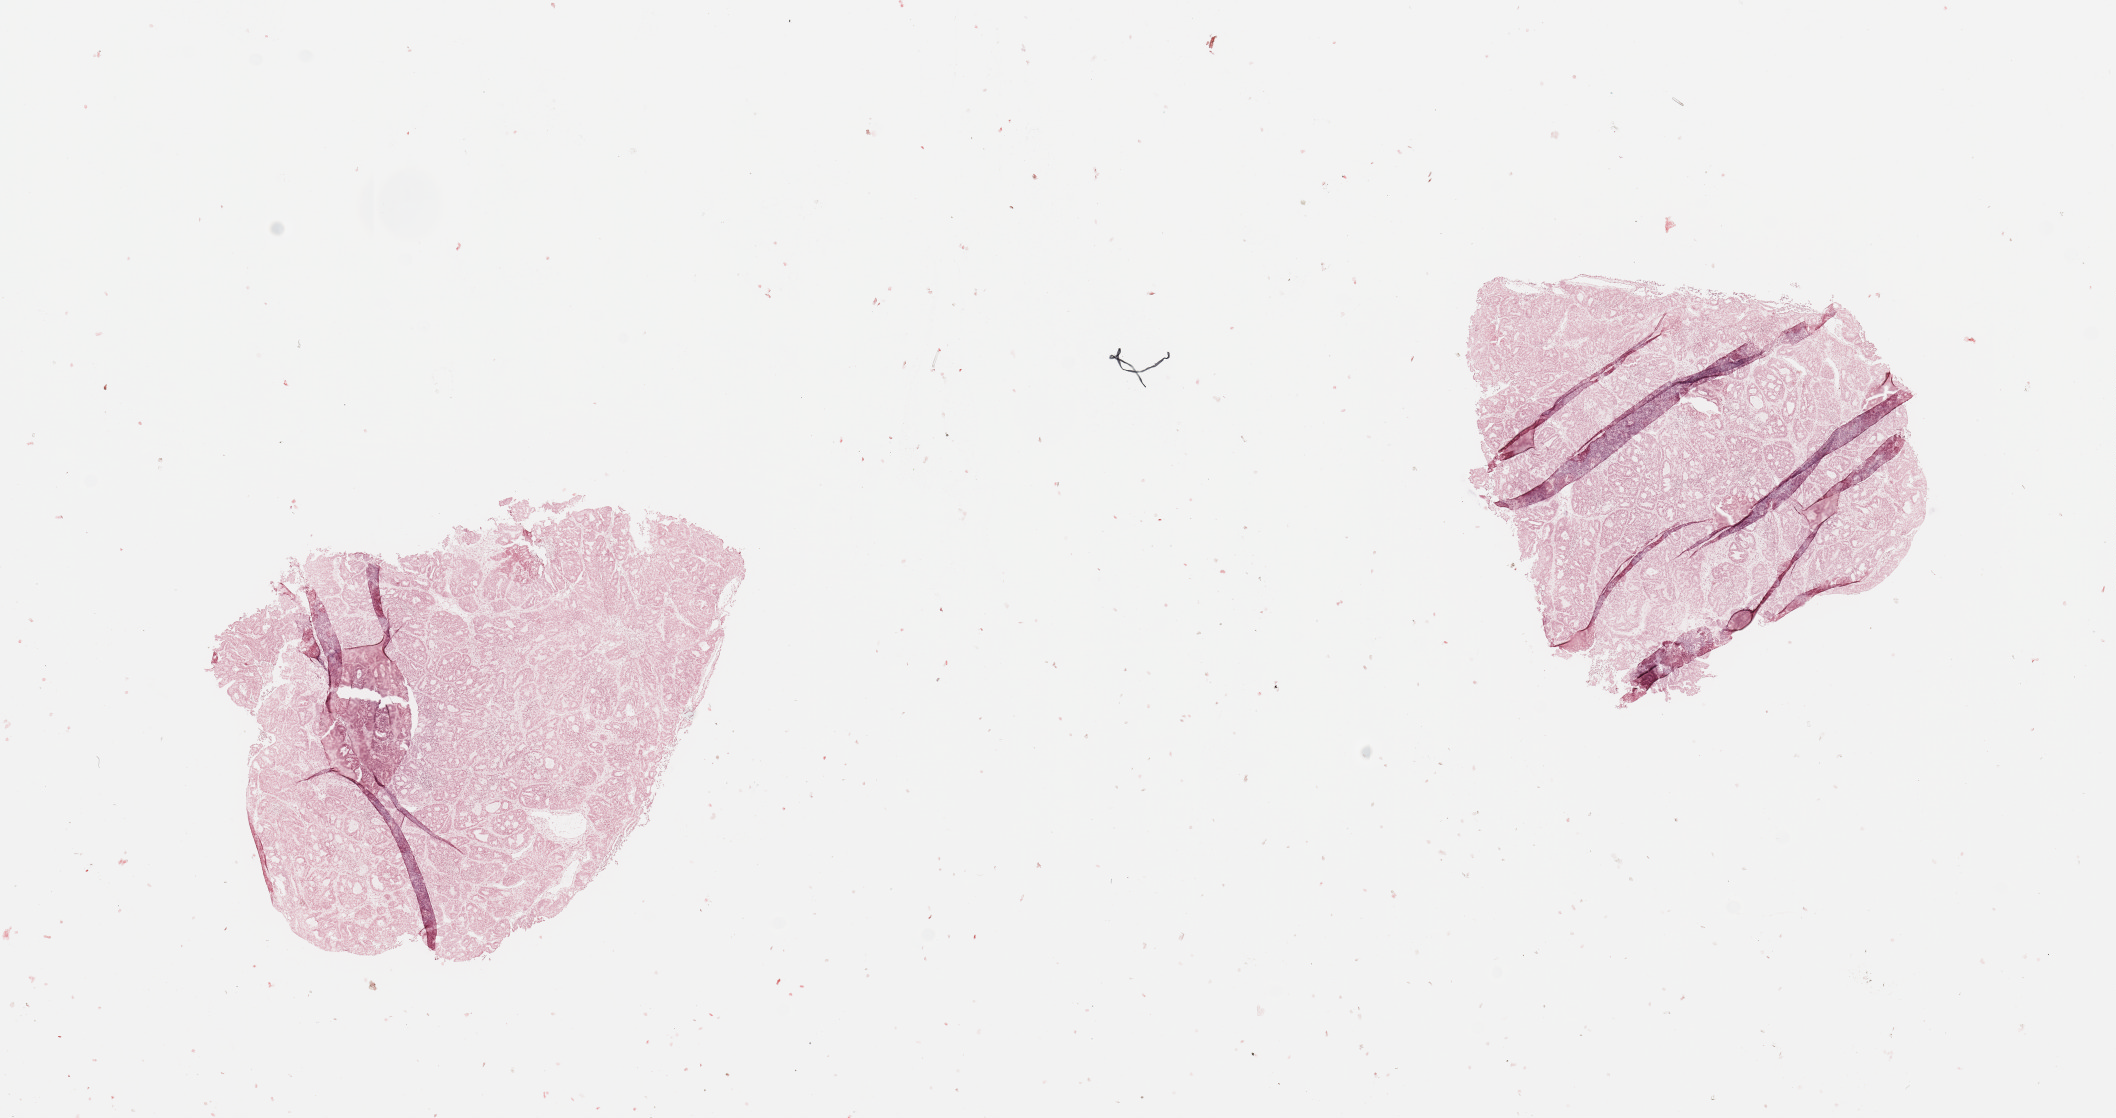
Digitized Hematoxylin and eosin (H&E) stained tissue section (whole slide), whole scanned area (about 16.7 x 8.8 mm, from a 20x scan) shown as a low-resolution overview; tumour tissue sample, sampled site: uterus. Patient: female, age 83 years. Histologic grade: G2 (moderately differentiated). Composition of this section per pathologist review: tumour nuclei 90%, necrosis 1%.
Diagnosis: Endometrioid adenocarcinoma, NOS. Primary tumour site (as recorded): posterior endometrium. AJCC pathologic stage: II.